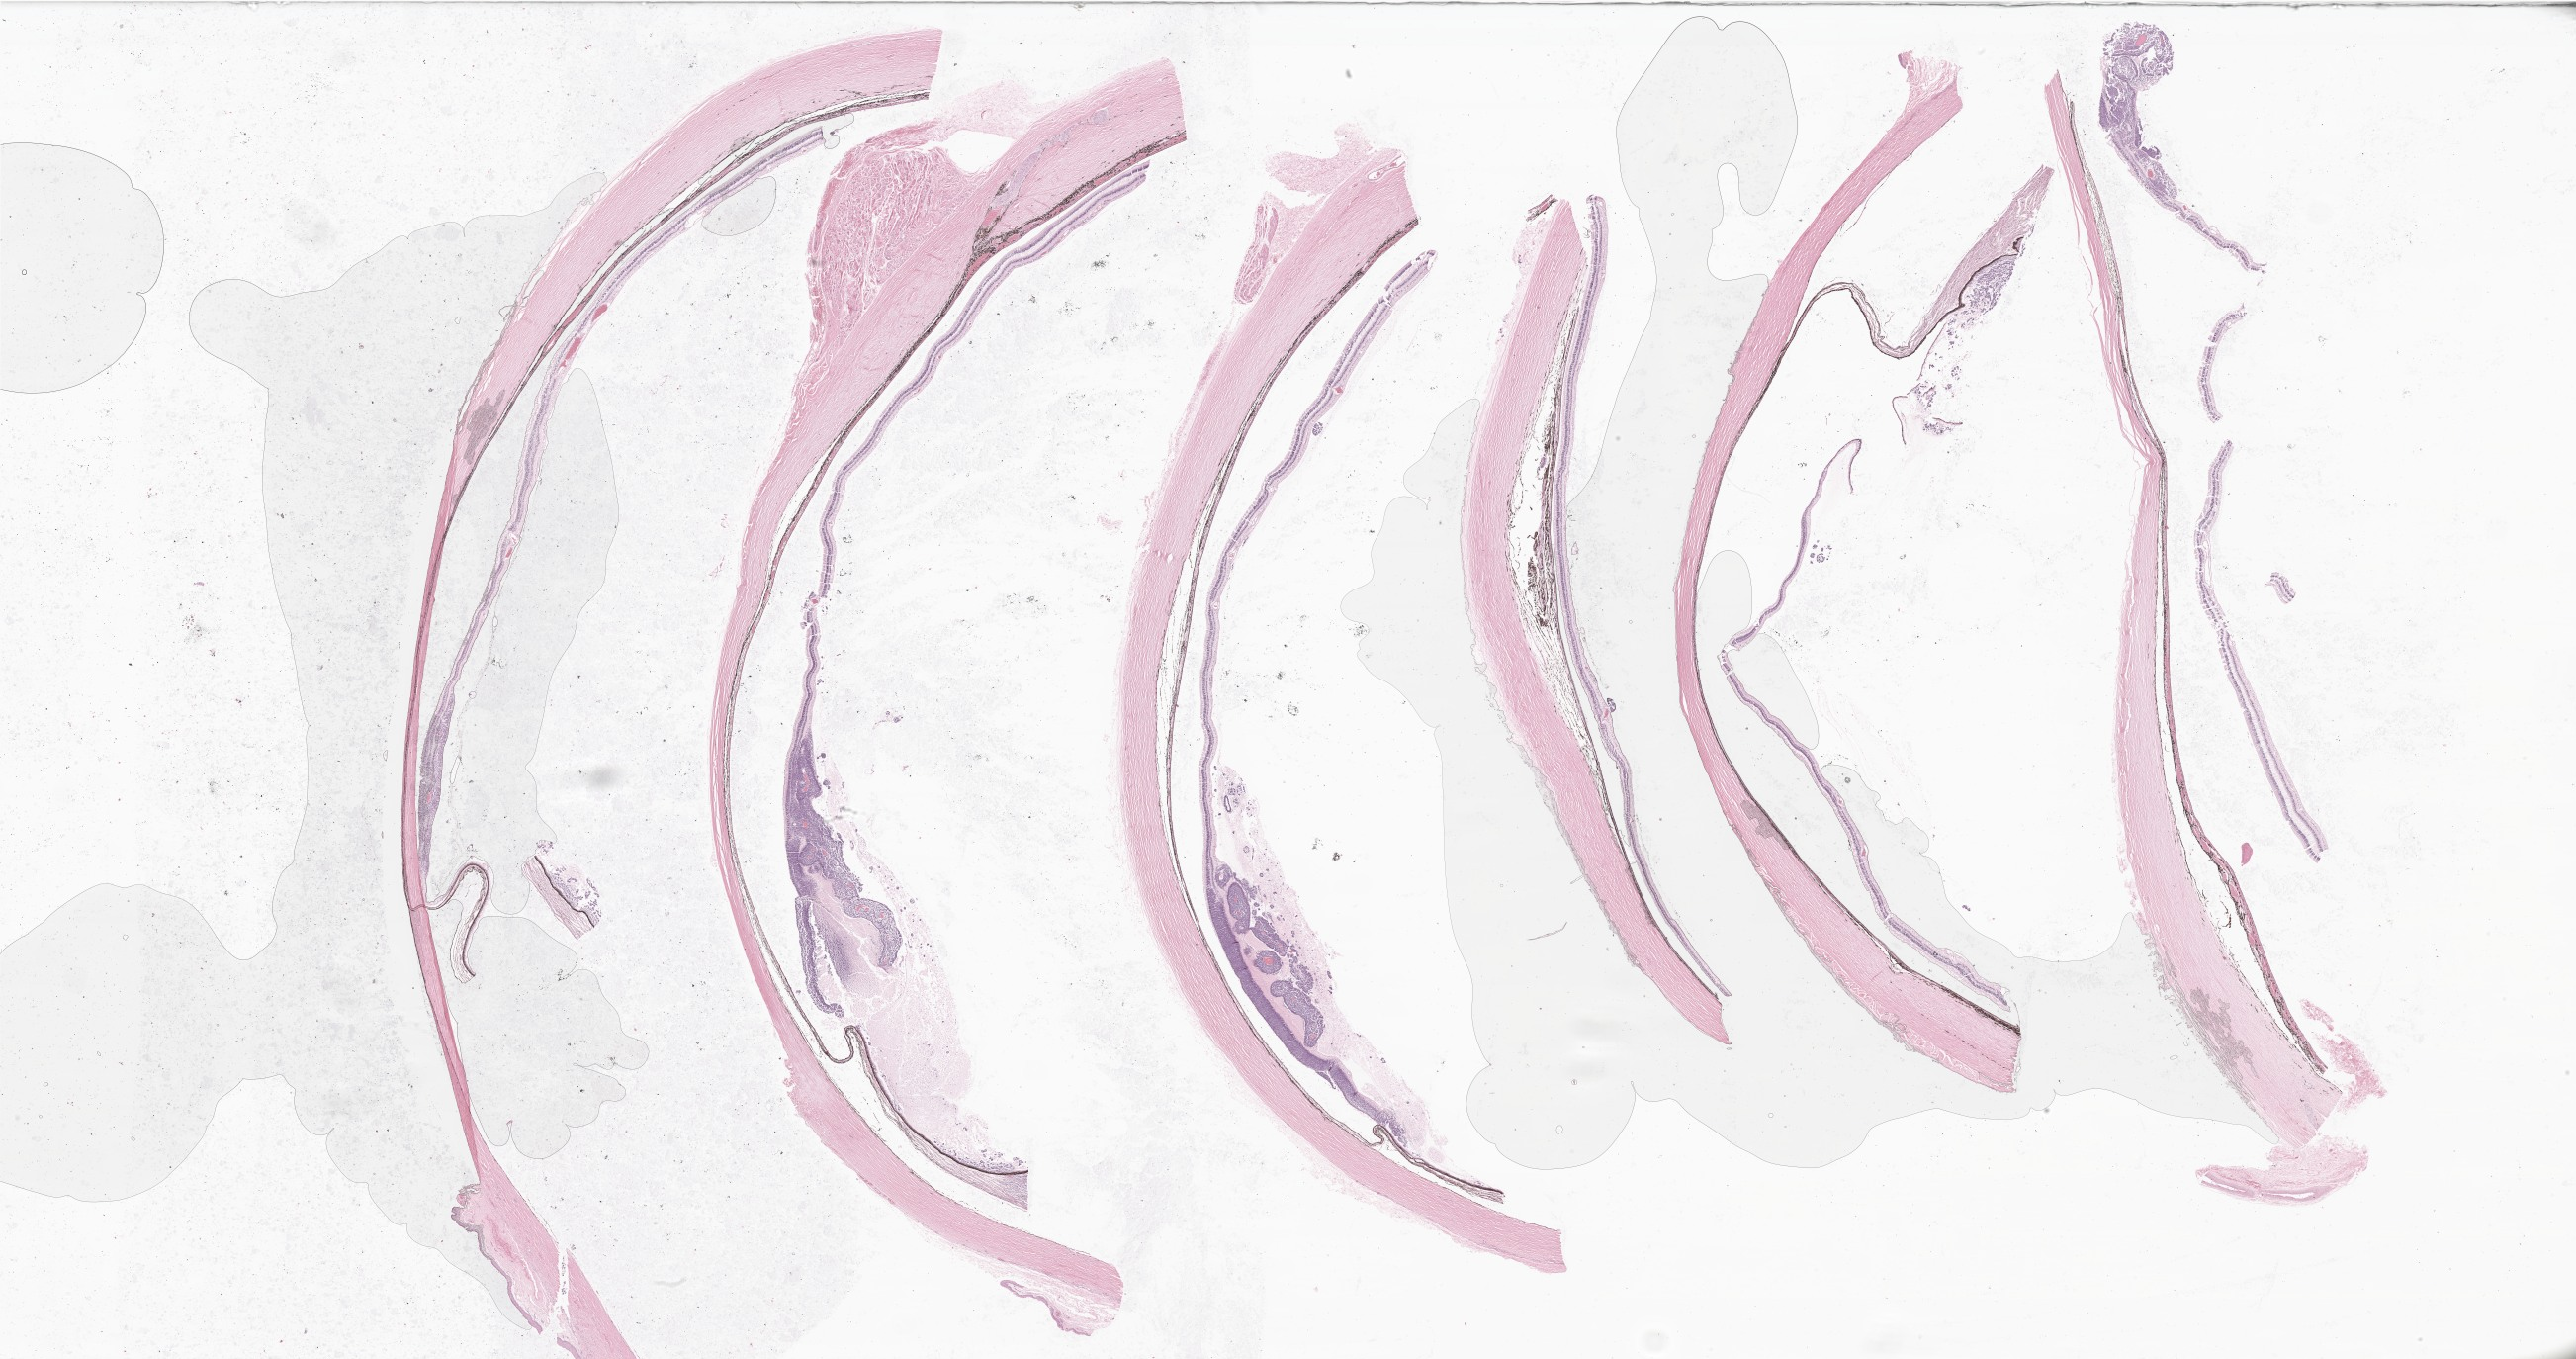
Digitized haematoxylin and eosin-stained section of tumor tissue from the eye, shown as a low-resolution overview of the whole scanned area (about 43.9 x 23.2 mm), formalin-fixed, paraffin-embedded (FFPE) tissue. Patient: male, age 80 months (6 years 8 months).
* recorded diagnosis: Retinoblastoma, diffuse